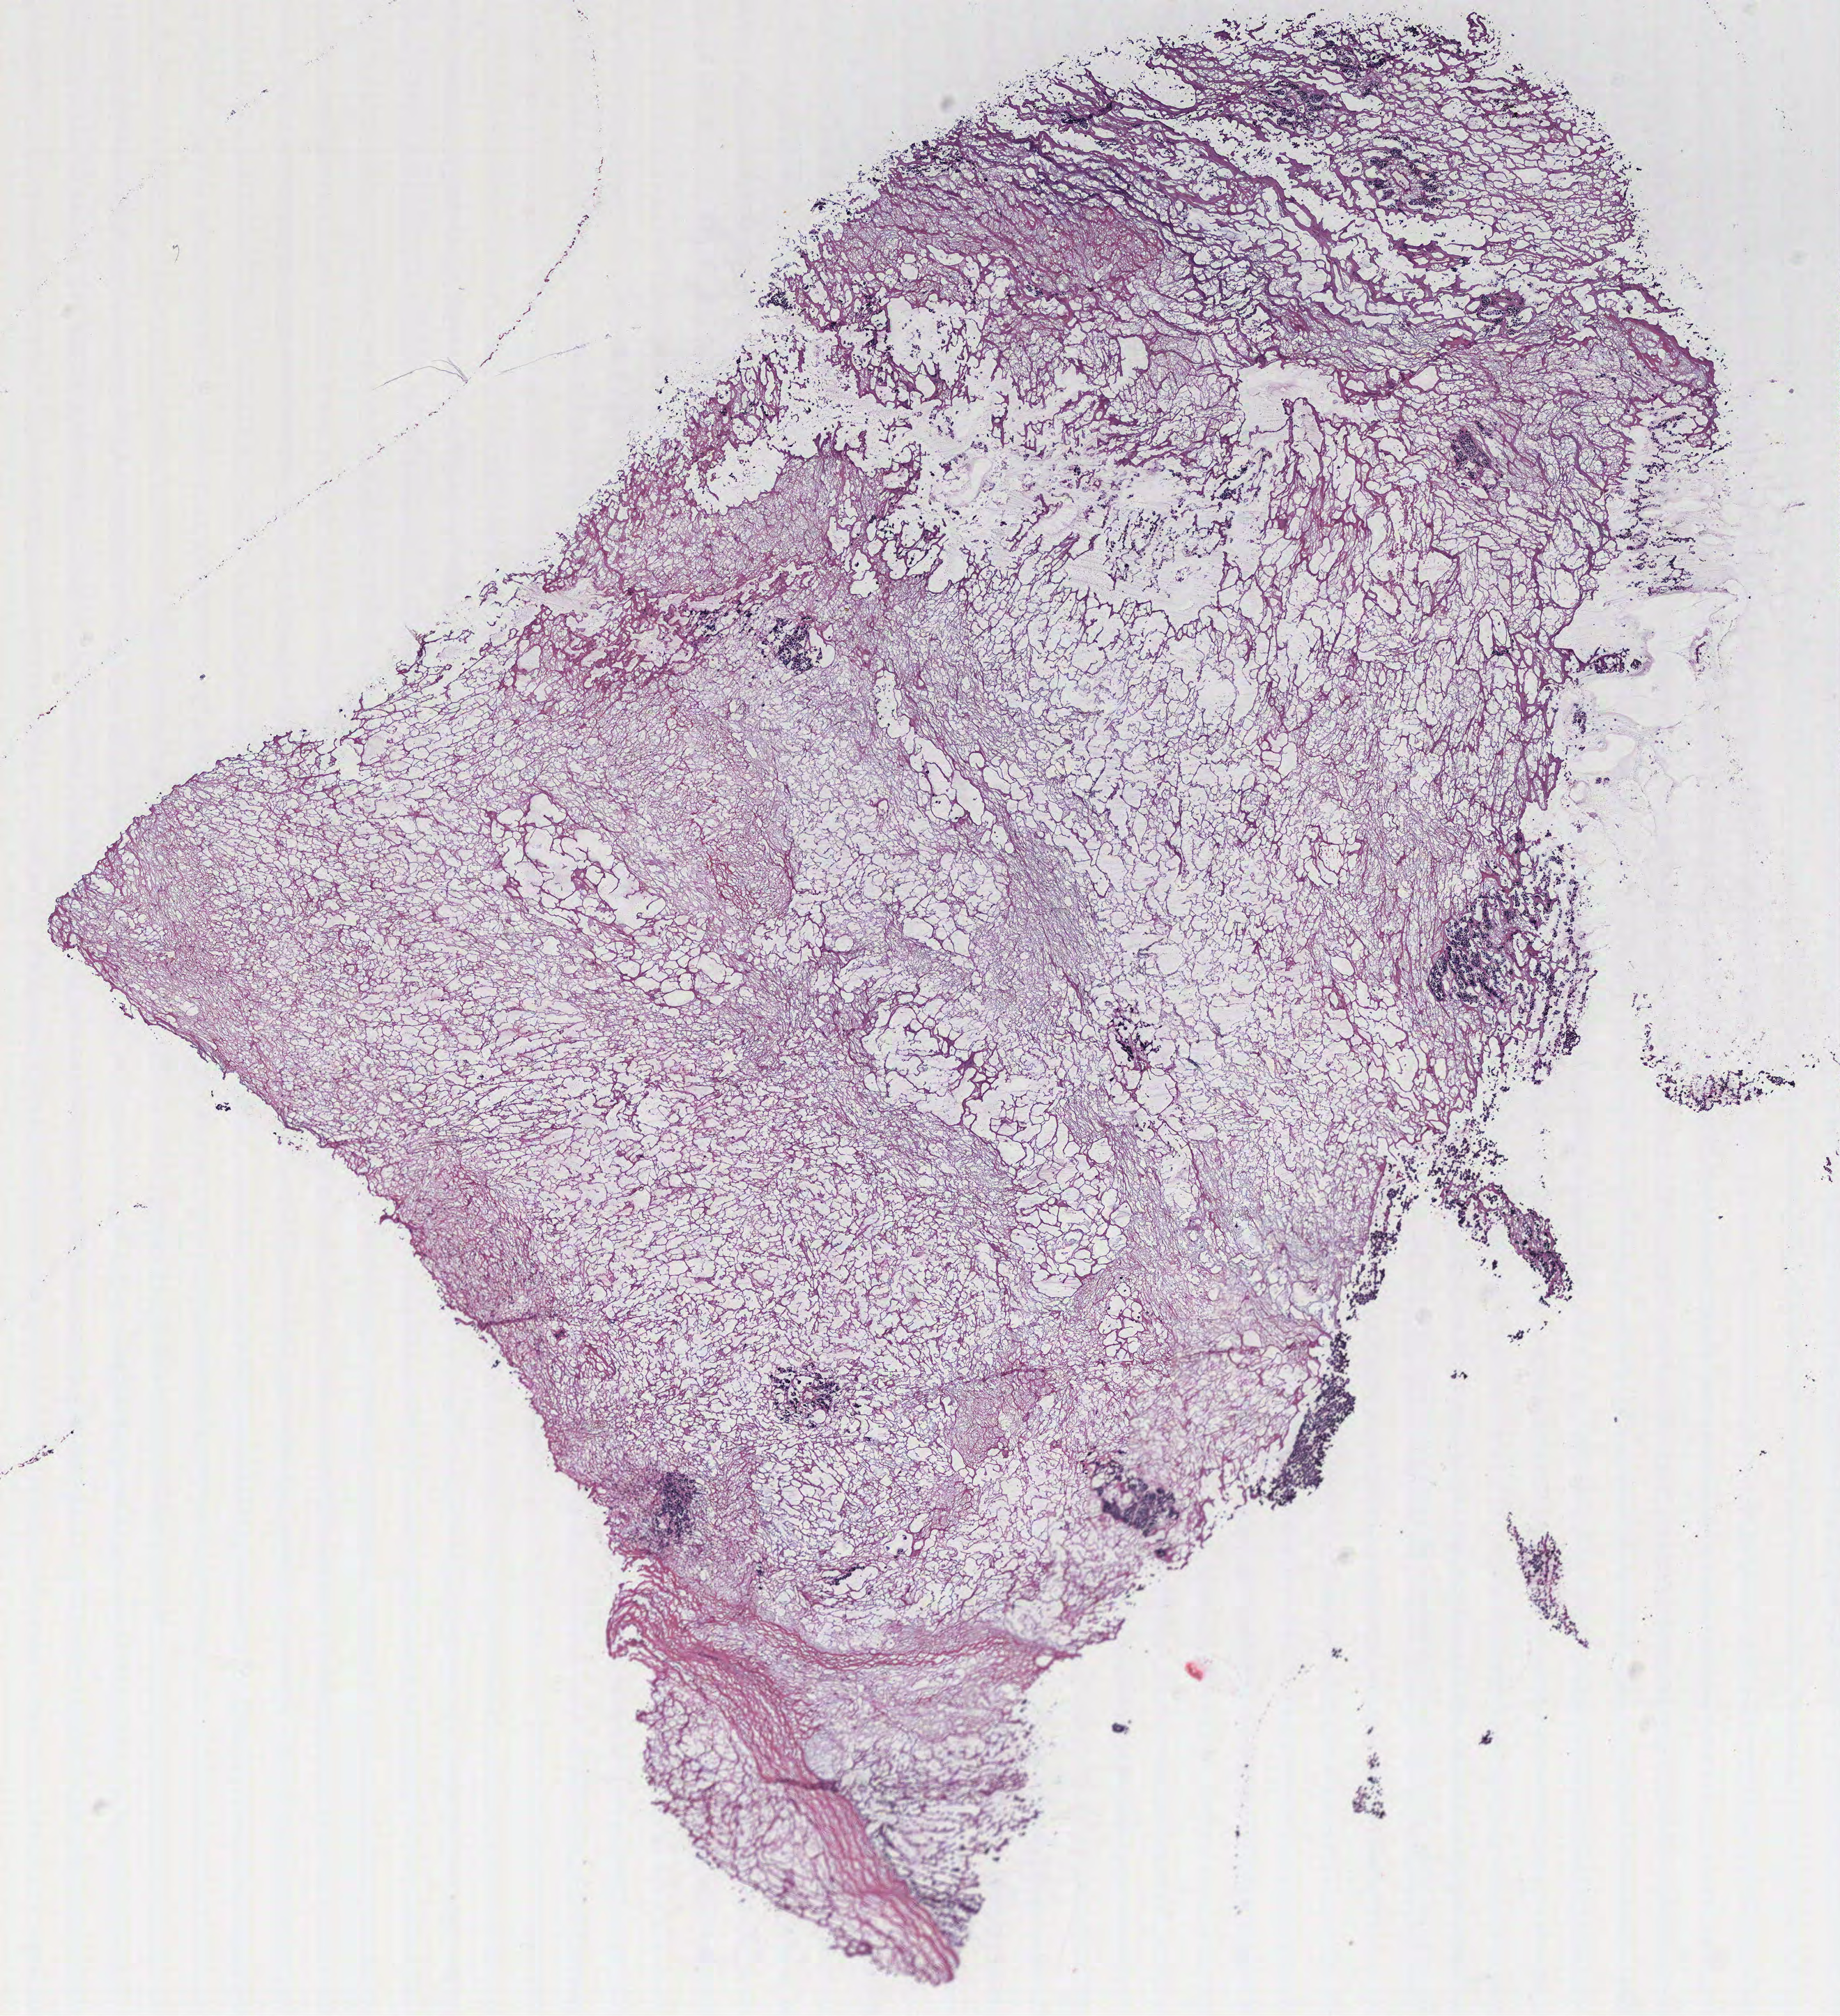
Whole-slide histology image, Hematoxylin and eosin (H&E) stained — low-resolution overview of the scanned area, about 10.6 x 11.6 mm, tumour tissue sample, ovary. Patient: female, age 57 years.
Primary tumour site (as recorded): ovary. Diagnosis: Serous adenocarcinoma, NOS.